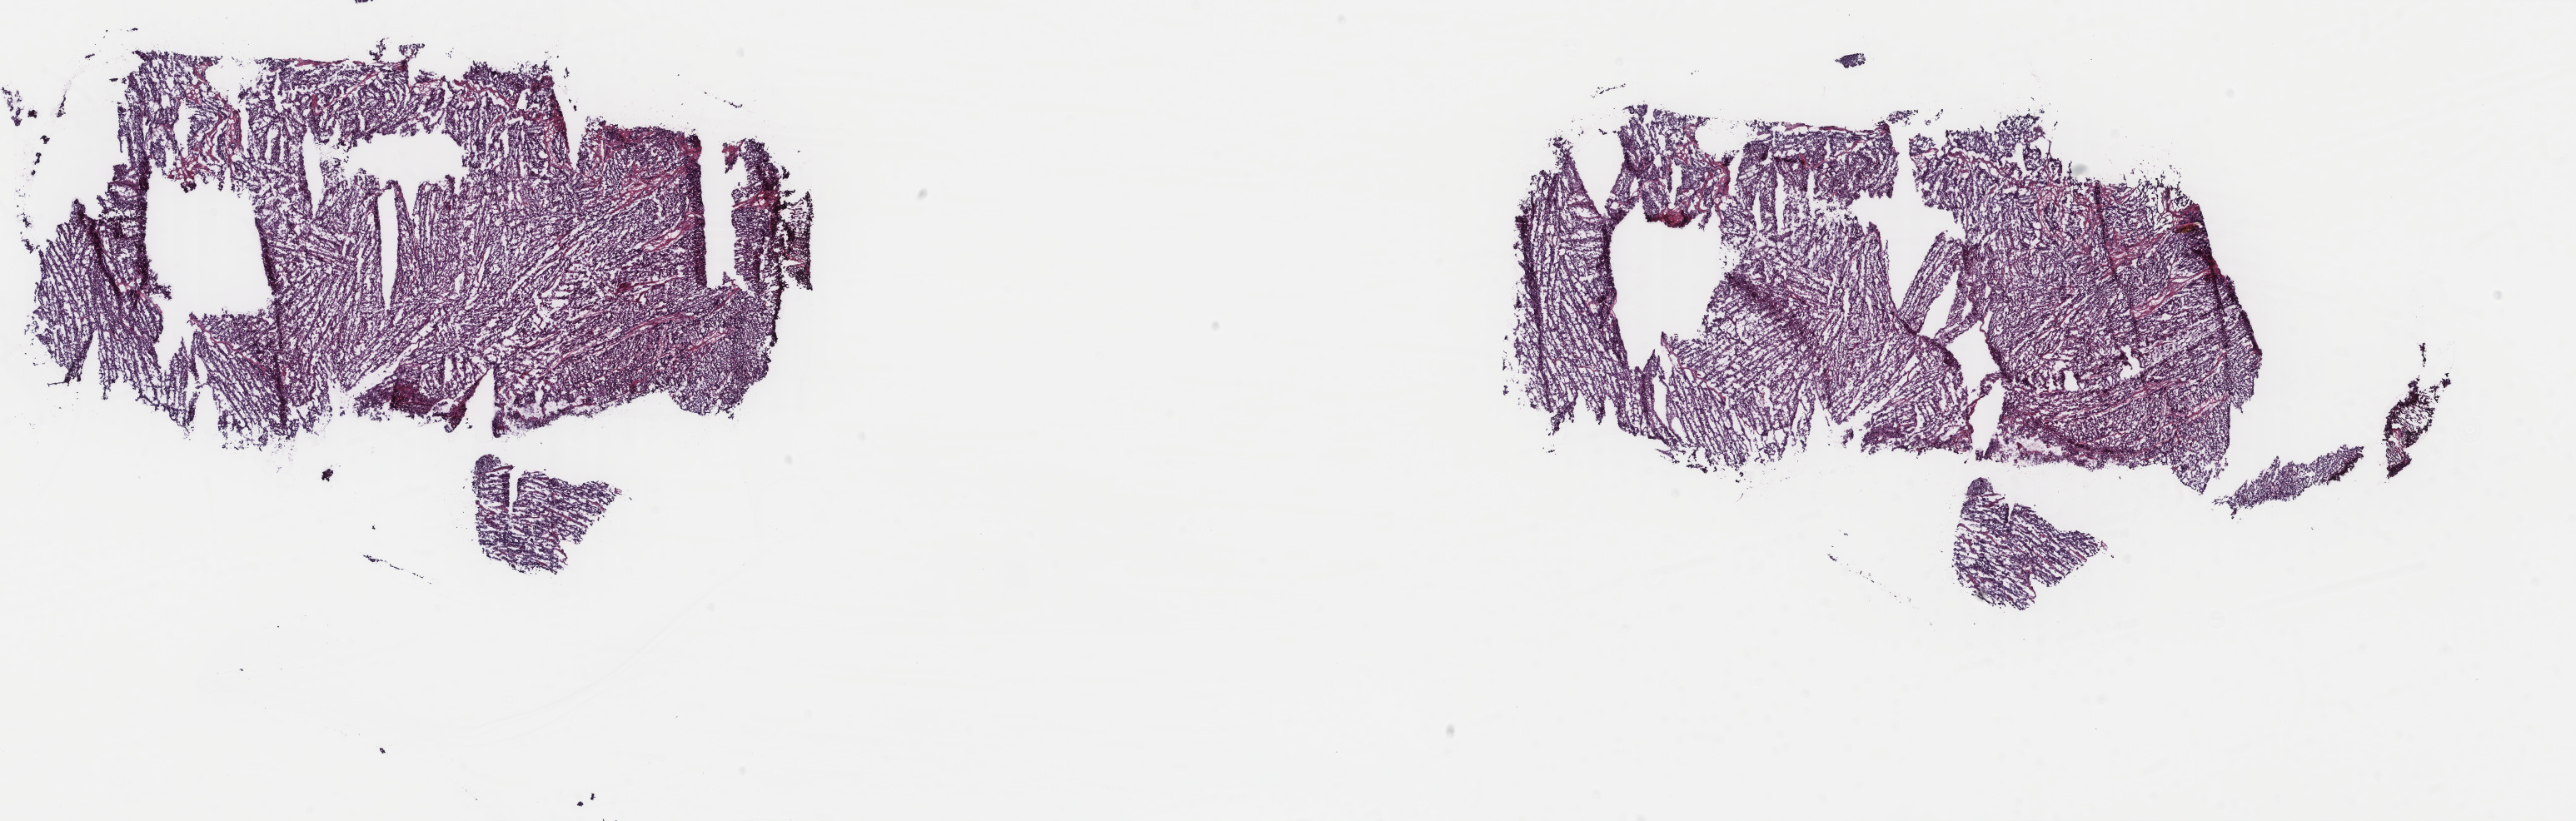
Digitized H&E tissue section (whole slide) — low-resolution overview of the scanned area, about 24.6 x 7.8 mm, frozen section from the top of the tissue portion, primary tumour sample from the uterus. Female patient; age at initial diagnosis 68 years. Histologic grade: G3 (poorly differentiated). Slide review estimates, as recorded: tumour cells 98%, tumour nuclei 80%, normal cells 0%, stromal cells 0%, necrosis 2%. Inflammatory infiltration, as recorded: lymphocyte infiltration 1%, monocyte infiltration 0%, neutrophil infiltration 0%.
• pathologic diagnosis: Adenocarcinoma with mixed subtypes (endometrium)
• FIGO stage: IIIC1